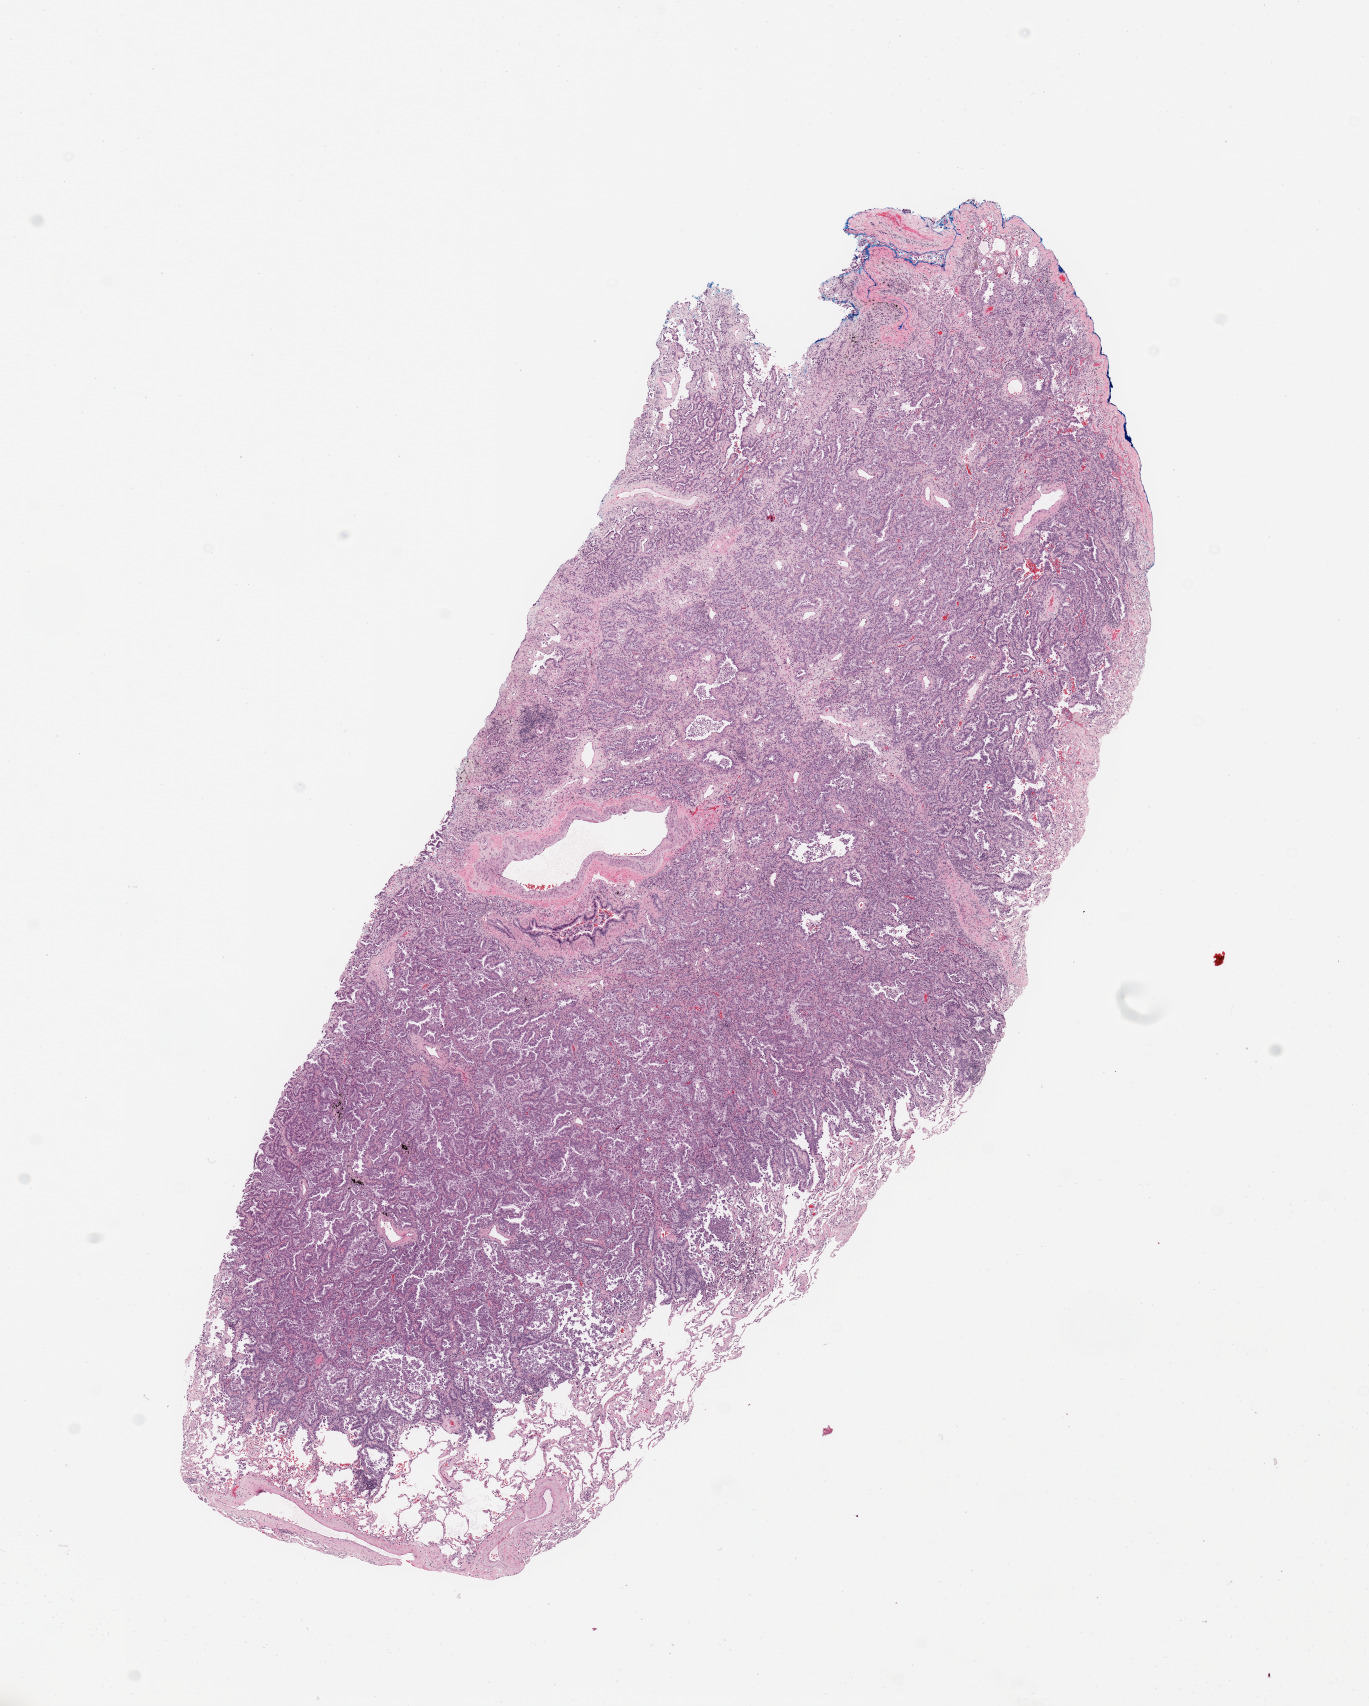
Digitized H&E tissue section (whole slide) — low-resolution overview of the scanned area, about 10.8 x 13.5 mm (from a 20x scan), tumour tissue sample, sampled site: lung. Patient: female, age 67 years. Histologic grade: G1 (well differentiated). Slide review estimates, as recorded: tumour nuclei 75%, necrosis 5%.
- diagnosis: Adenocarcinoma, NOS
- AJCC pathologic stage: IA
- primary tumour site (as recorded): left upper lobe